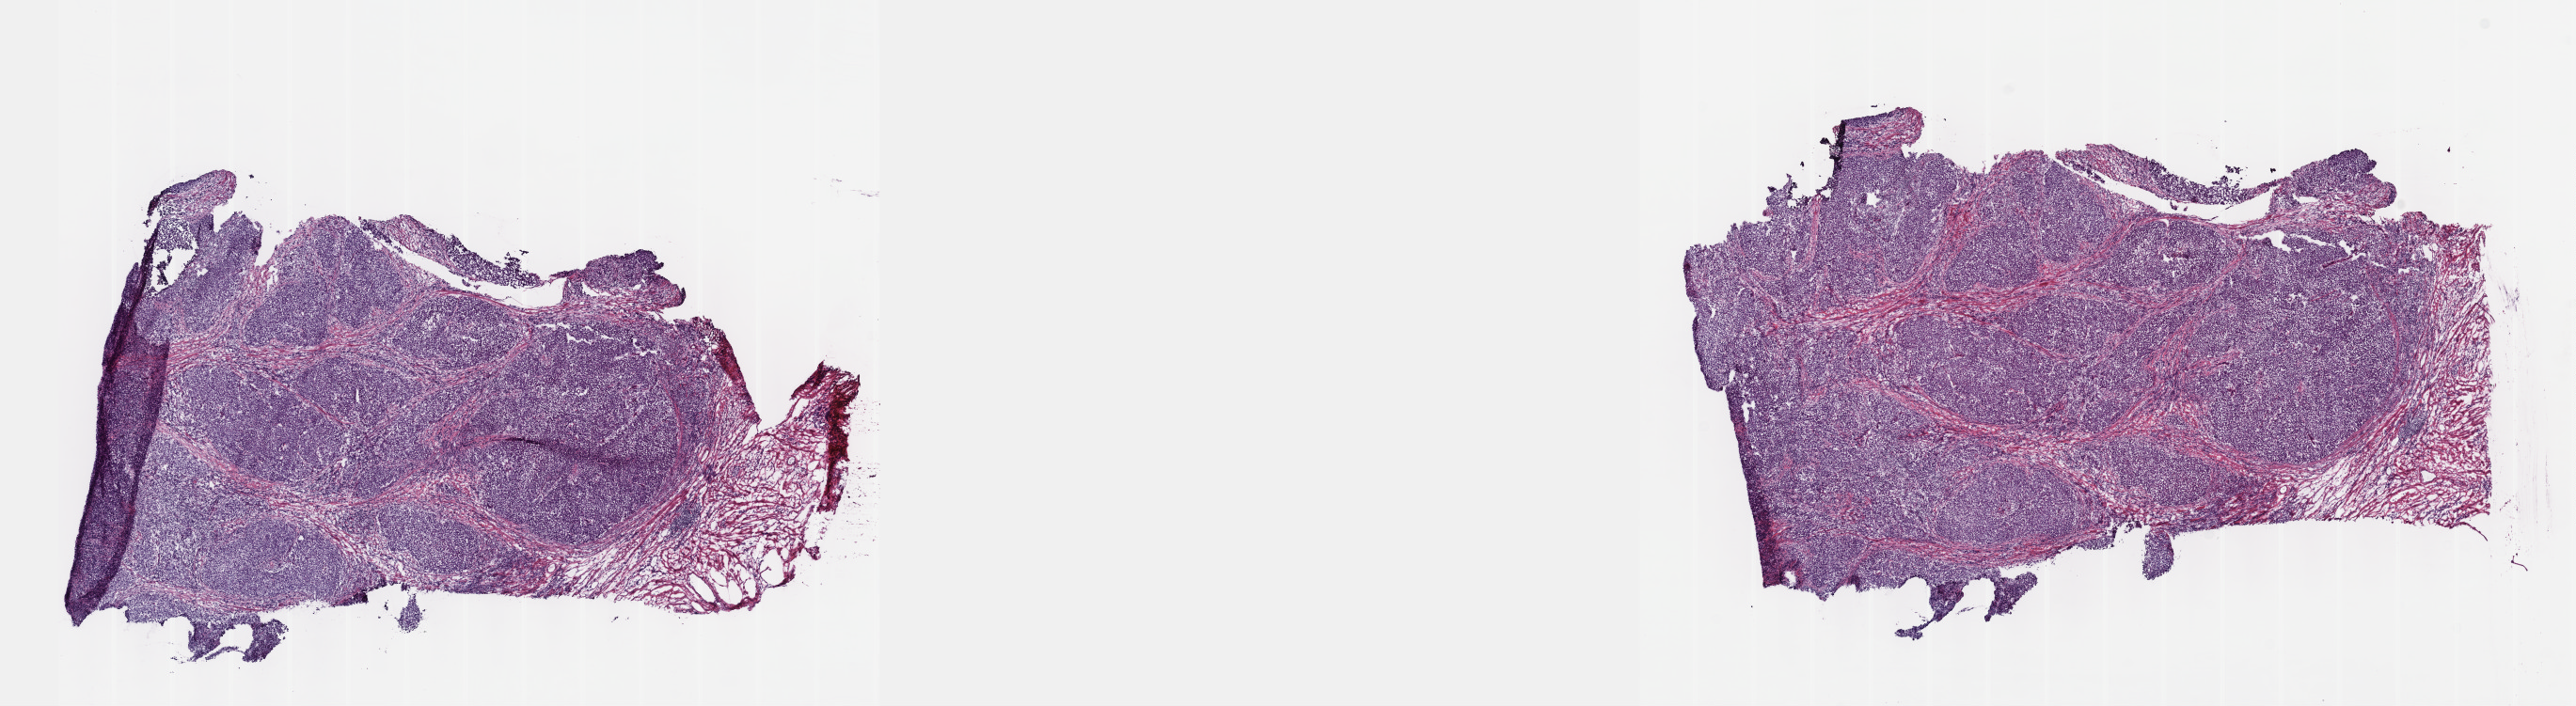
Digitized H&E-stained tissue section (whole slide), low-resolution overview of the scanned area, about 22.1 x 6.1 mm. Frozen section. Bladder, primary tumour sample. Female patient; age at initial diagnosis 78 years.
Histologic diagnosis: Transitional cell carcinoma.